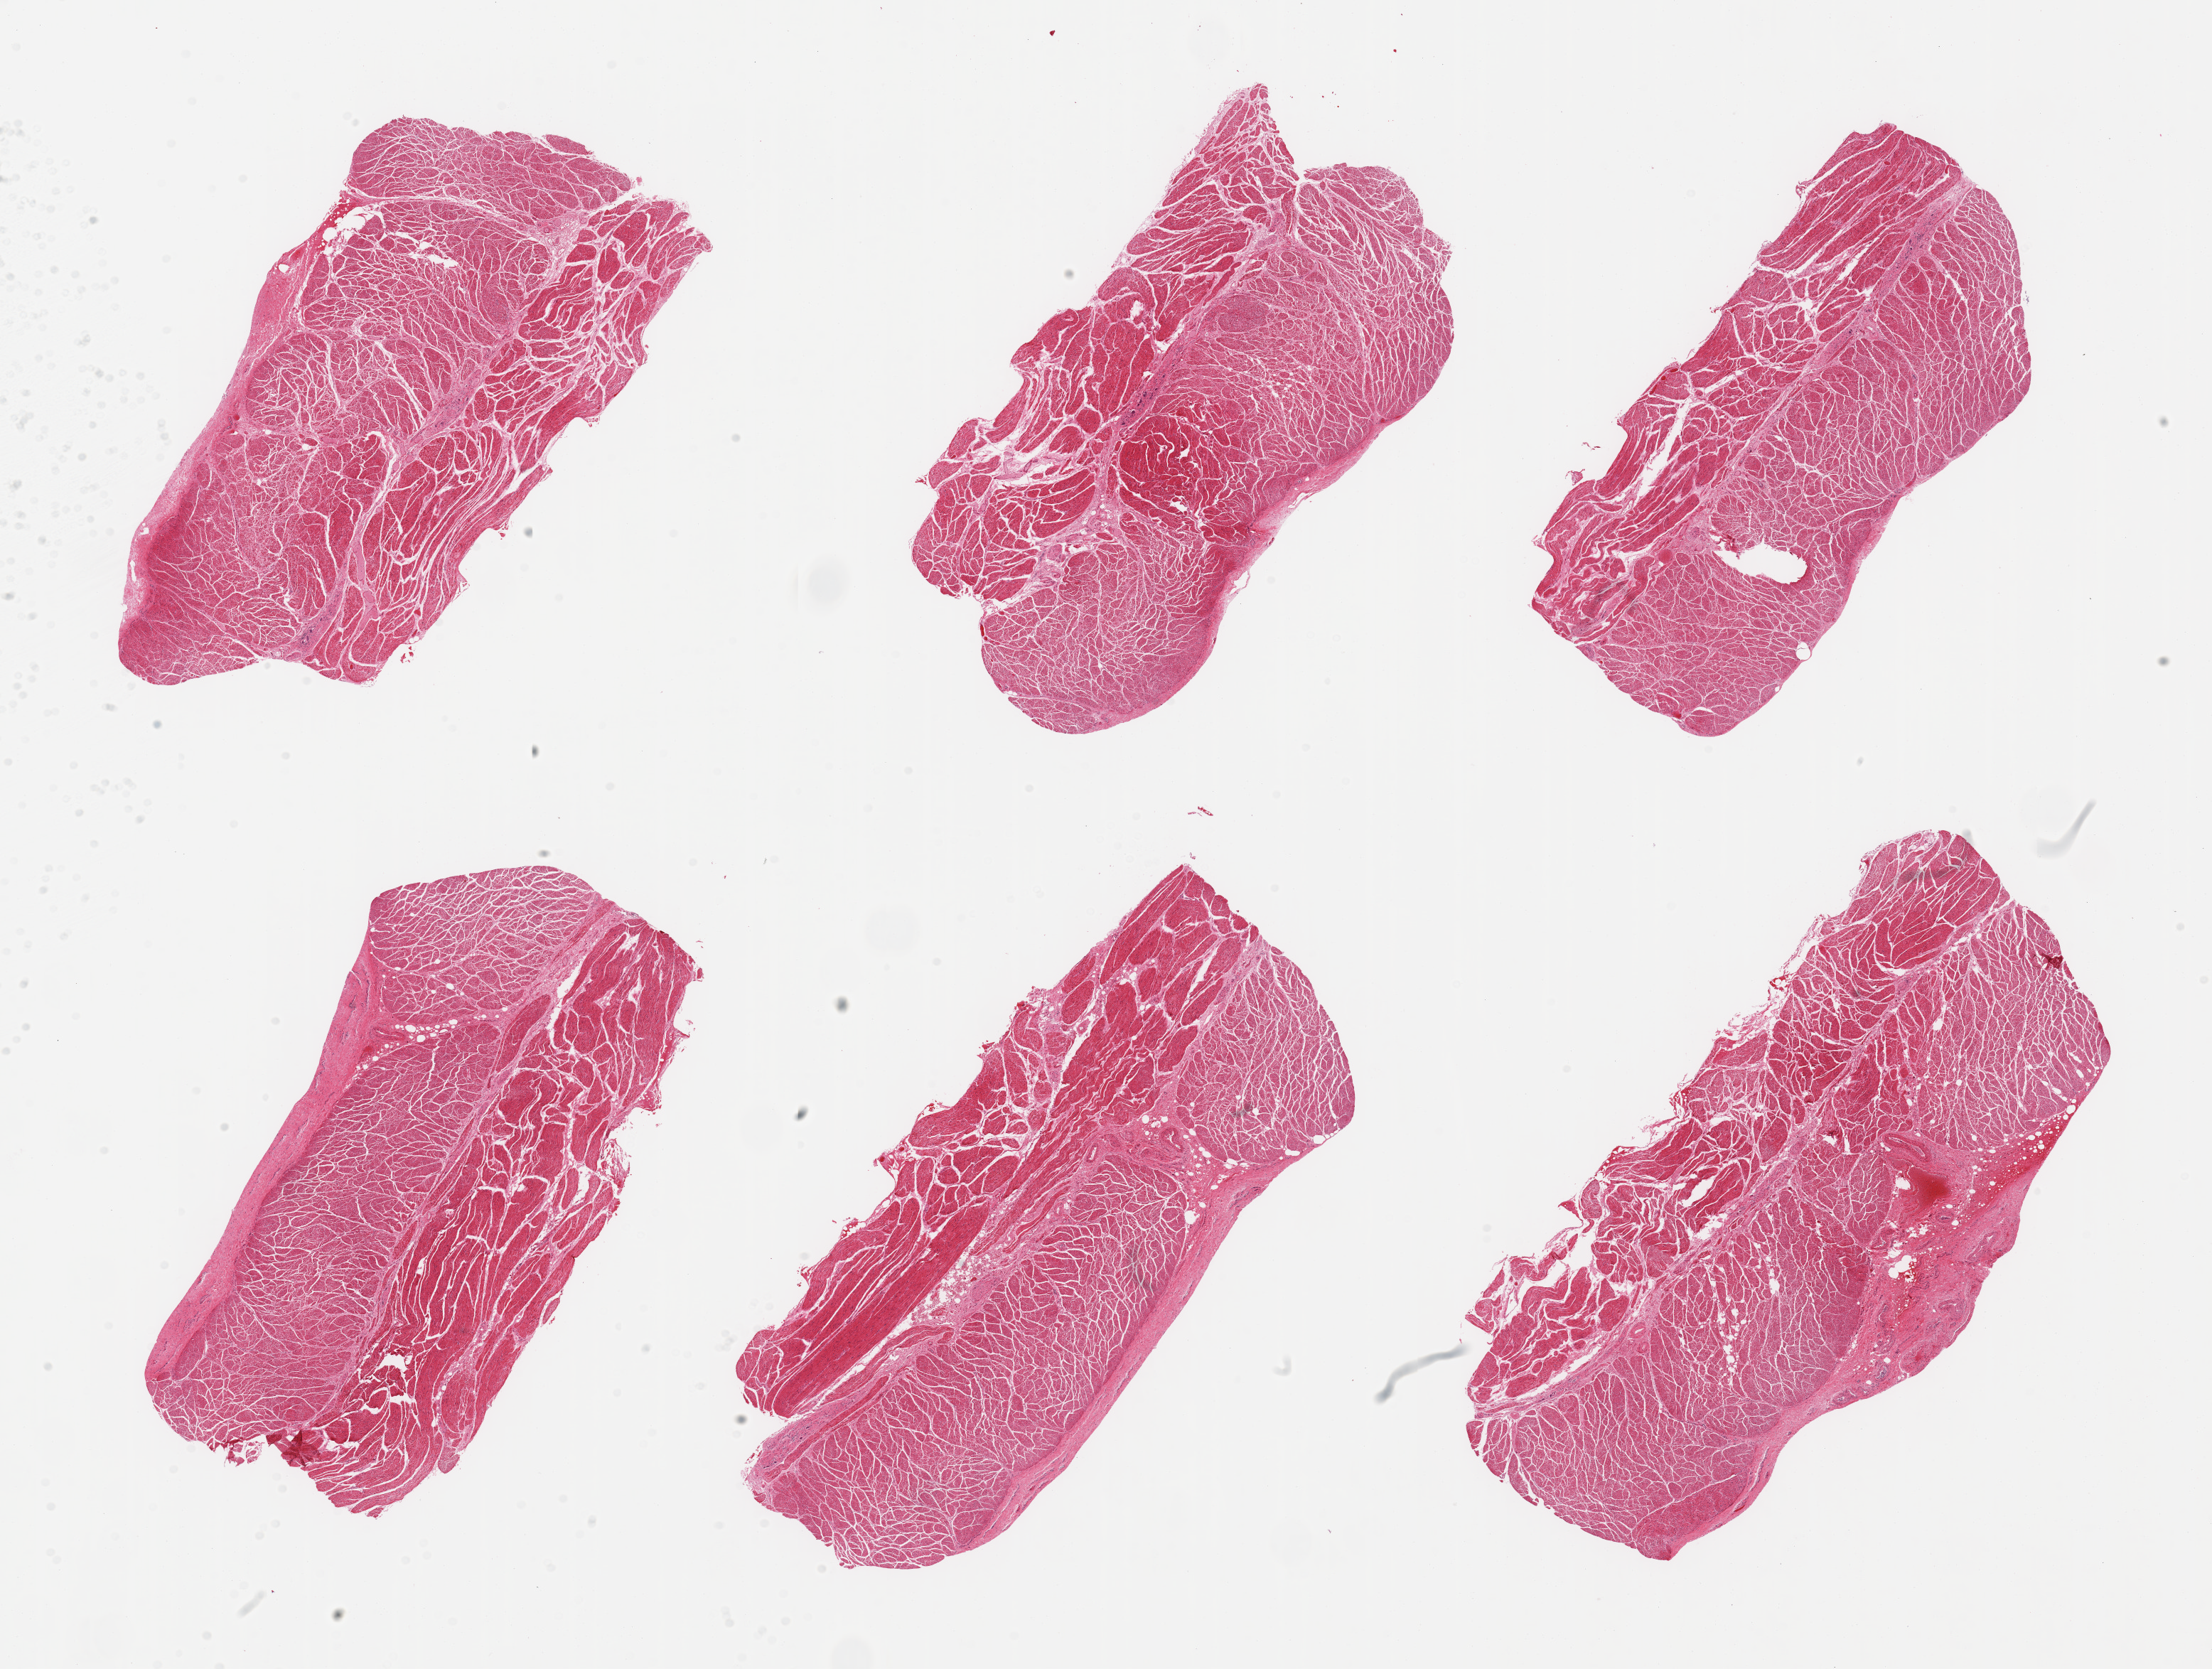
Whole-slide image, hematoxylin and eosin (H&E) stain, low-resolution overview of the scanned area, about 24.6 x 18.6 mm. PAXgene-fixed paraffin-embedded (PFPE) section. Section of esophageal muscle (target tissue). Donor tissue sample. Donor sex: male.
Review note (as recorded): 6 pieces, confirmed target muscularis.